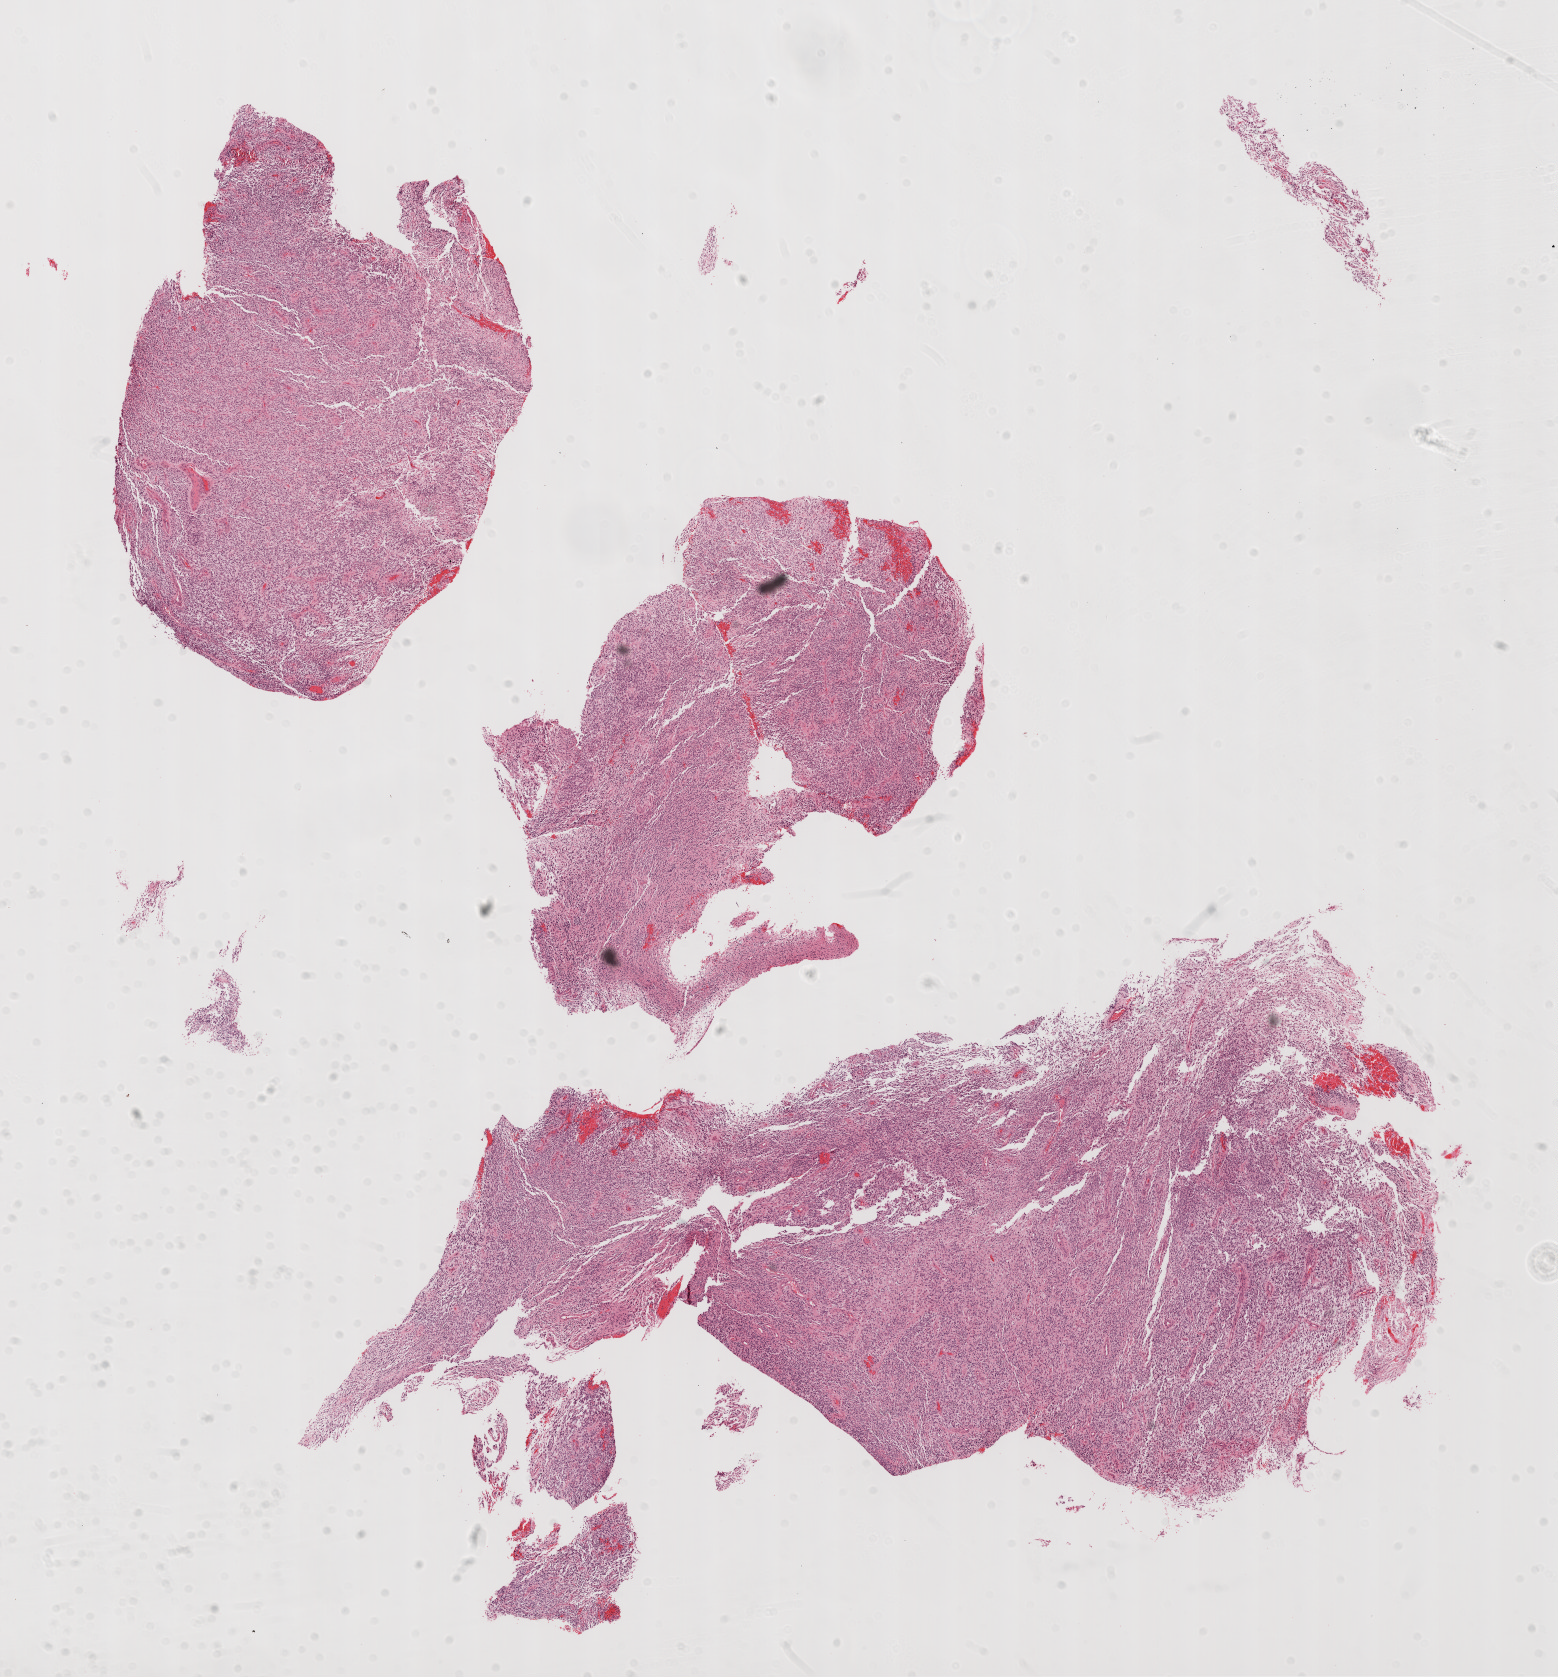
Whole-slide histology image, H&E — shown as a low-resolution overview of the whole scanned area (about 12.6 x 13.5 mm, acquisition: 20x scan). FFPE section. Primary tumour sample from the brain. Male patient; age at initial diagnosis 65 years.
Pathologic diagnosis: Glioblastoma.